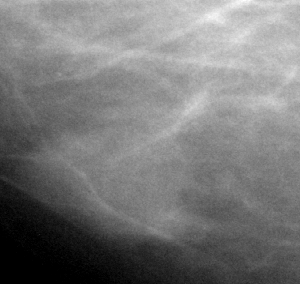
Cropped region of a digitized screen-film mammogram centred on a radiologist-marked abnormality, right breast, MLO view.
Finding: mass, shape oval, margins circumscribed; BI-RADS assessment category 3; benign without callback (not worked up further).